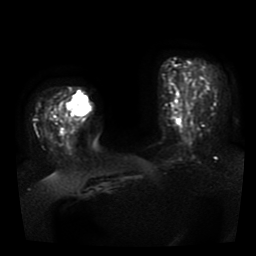
Breast MRI, one axial slice; position 14 of 41 along the scan axis; diffusion-weighted series; image 2 of 4 stored at this slice position (different b-values; order by instance number); 1.5 T; 5 mm slice thickness; 256 × 256 image matrix, field of view 330 × 330 mm. Female patient.
Structures marked on this image (expert manual segmentation):
- tumour on diffusion-weighted imaging: bounding box [x1, y1, x2, y2] px = [62, 93, 90, 116]